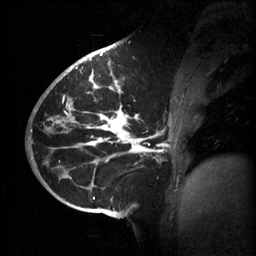
Breast MRI (dynamic contrast-enhanced), one sagittal slice; position 30 of 60 along the scan axis; 3 images stored at this slice position (order not interpretable as contrast timing); 1.5 T; TE 4.2 ms, TR 11 ms; 2 mm slice thickness; 256 × 256 image matrix, field of view 220 × 220 mm. Patient: female, 51 years.
Outlined on this slice (semi-automatically segmented with operator editing):
- analysis volume of interest (the breast-tissue region the enhancement analysis was run in; not a lesion): box from (x=63, y=80) to (x=175, y=201) px
- tumour enhancement mask (voxels above the 70 % enhancement threshold inside the analysis volume of interest): (x=63, y=80)–(x=164, y=199)